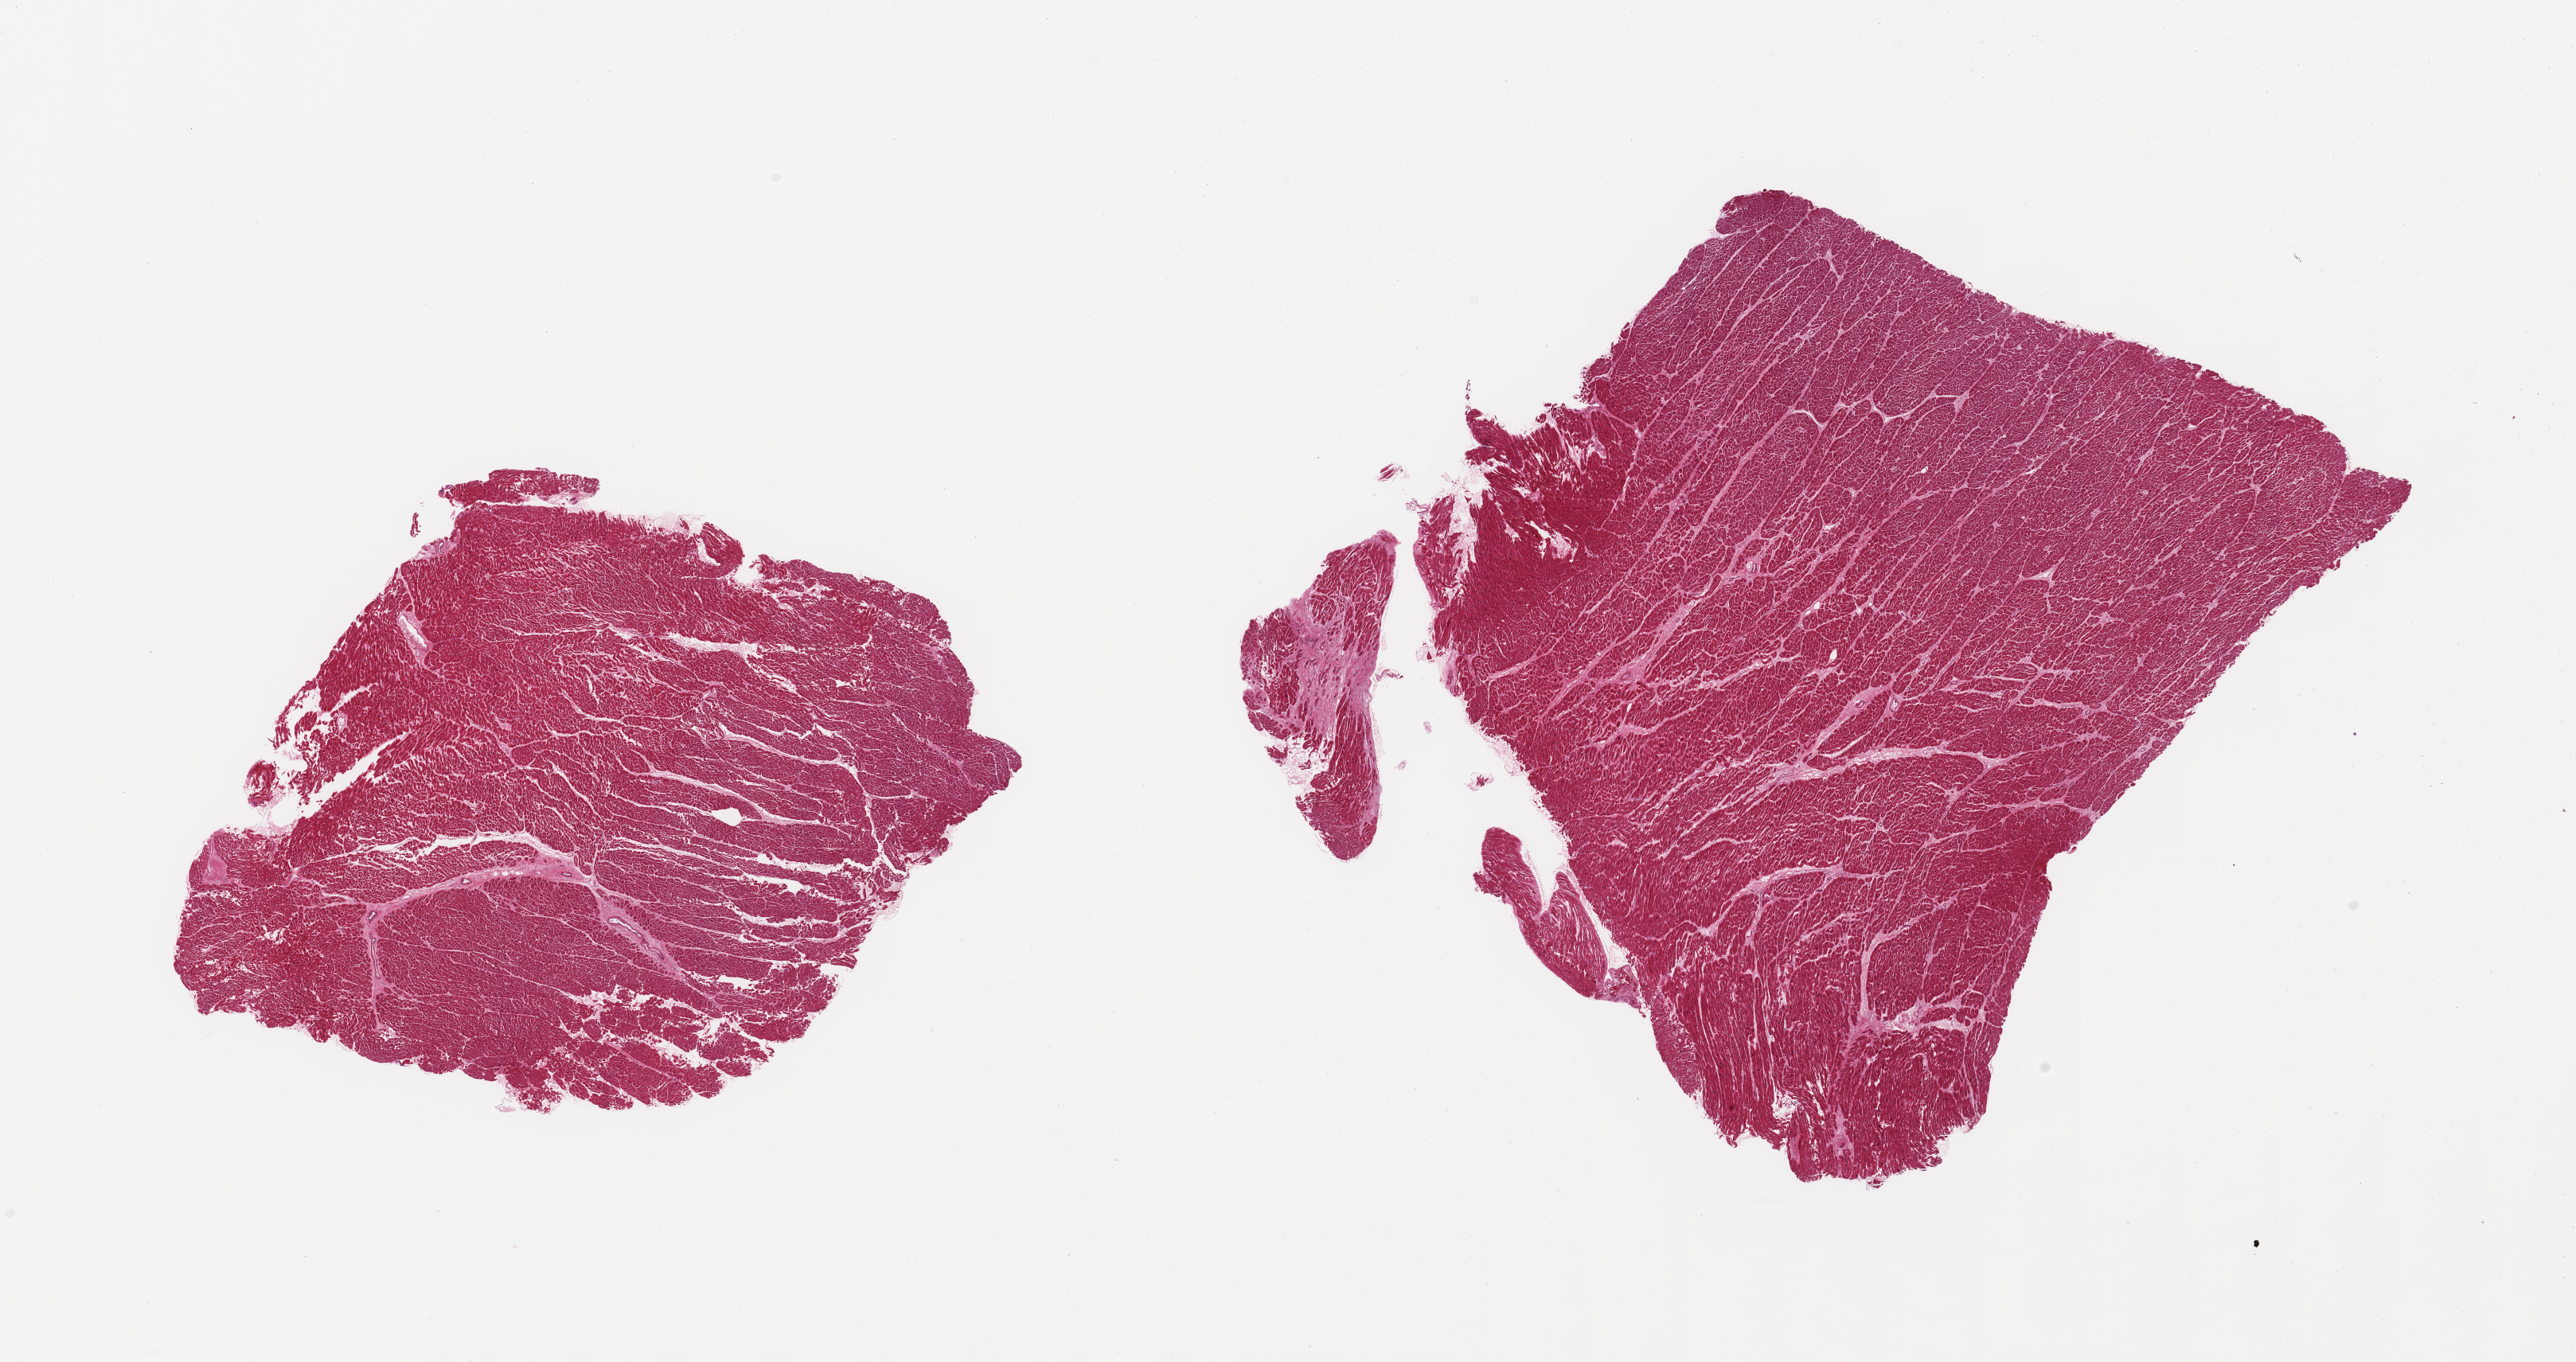
Hematoxylin and eosin (H&E) whole-slide image, brightfield — shown as a low-resolution overview of the whole scanned area (about 25.6 x 13.5 mm); PAXgene-fixed, paraffin-embedded tissue; target tissue: heart; donor tissue sample. Donor sex: male.
Pathologist's review note for this sample: 2 pieces; interstitial fibrosis with focal scarring; ? focal edema of fibers and eosinophilia suggestive of early infarction.